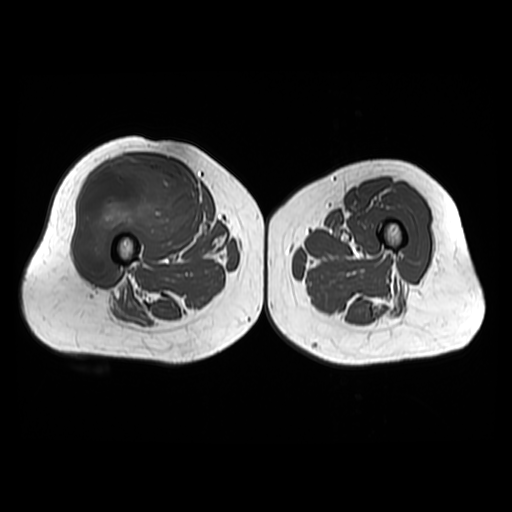
MRI of an extremity soft-tissue mass, one axial slice; slice 28 of 48 in the series (ordered by position); 512 × 512 image matrix, field of view 440 × 440 mm. Female patient. From the clinical record (not read from this slice): histological type: pleiomorphic undifferentiated sarcoma; grade: high; site of the primary tumour: right quadricep.
Annotated regions visible in this slice (expert manual segmentation):
- gross tumour volume including surrounding oedema: bounding box (x1, y1, x2, y2) in pixels: (73, 156, 197, 277)
- gross tumour volume (mass): (73, 156, 197, 277)